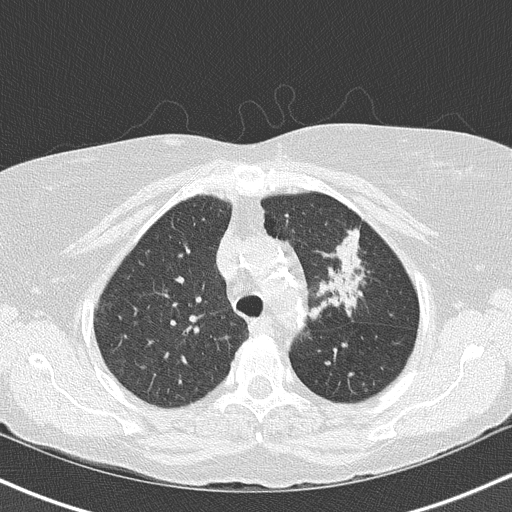
Chest CT (low-dose screening protocol), one axial image. Third annual screen. Lung window (W 1500 / L -600 HU). Female participant, aged 68 years at enrolment.
Expert-annotated lung lesion, bounding box [x1, y1, x2, y2] px = [299, 215, 383, 323]. The exam's reader record, not a measurement of the box and not confirmed to be the same lesion: non-calcified nodule or mass ≥4 mm, left upper lobe, 5 × 5 mm, poorly defined margins, mixed attenuation, pre-existing on the prior screen: yes; interval growth: yes. Official screen result: positive, other.